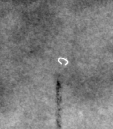
Cropped region of a digitized screen-film mammogram centred on a radiologist-marked abnormality; right breast; CC view; BI-RADS breast density category 3 (scale 1–4).
Calcifications, morphology round and regular / lucent centered; BI-RADS assessment category 2; benign; no additional work-up was recommended (benign without callback).